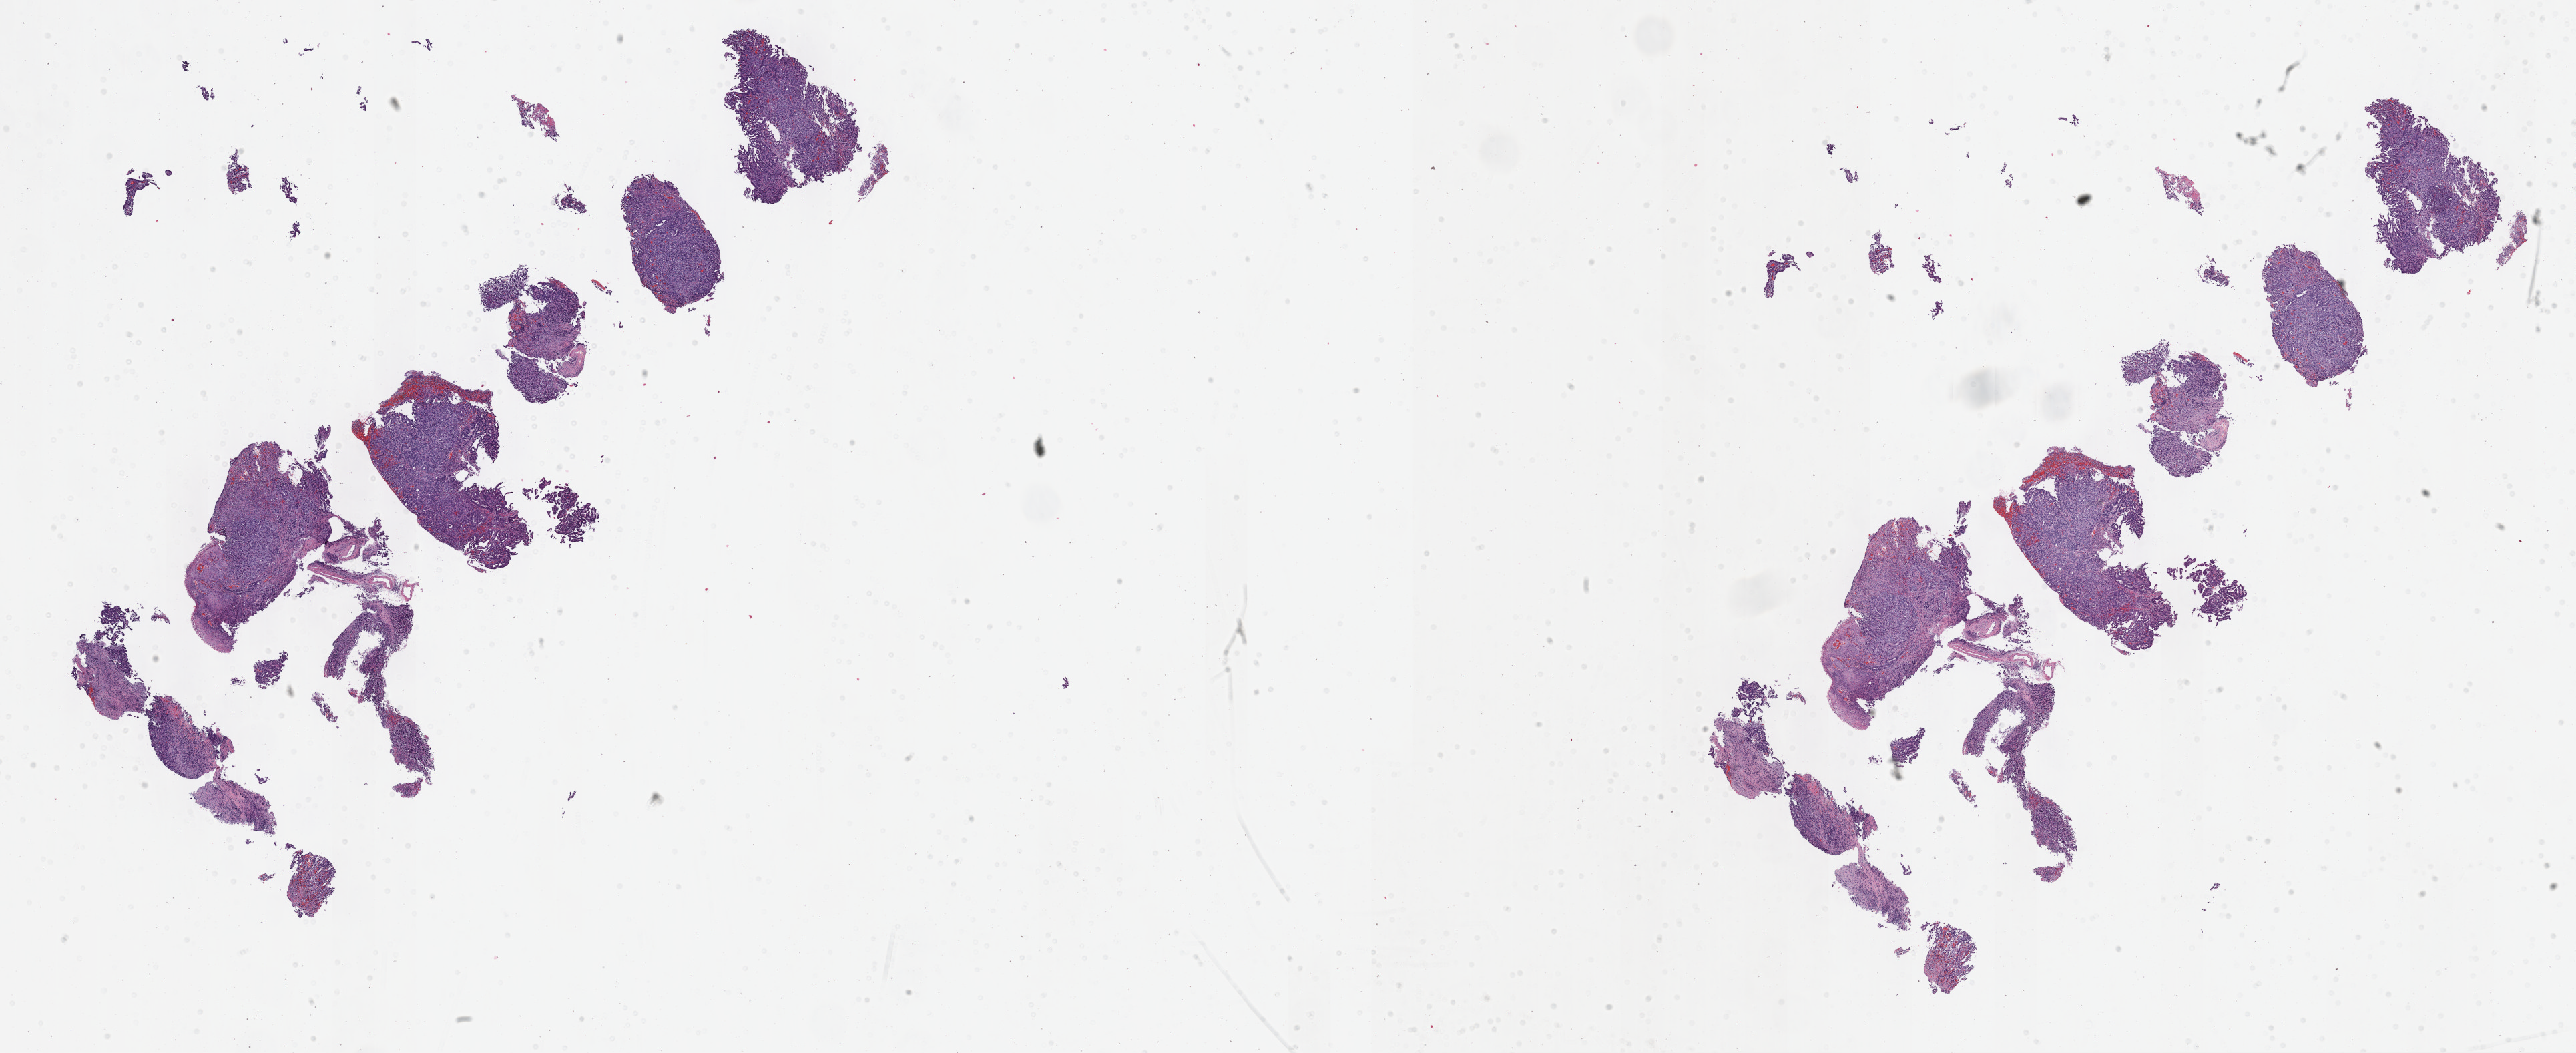
H&E whole-slide image, low-resolution overview of the scanned area, about 31.2 x 12.8 mm (acquisition: 40x scan). Formalin-fixed paraffin-embedded (FFPE) diagnostic section. Primary tumour sample from the esophagus. Male patient; age at initial diagnosis 60 years. Histologic grade: G3 (poorly differentiated). Composition of this section per pathologist review: tumour cells 80%, tumour nuclei 80%, normal cells 0%, stromal cells 20%, necrosis 0%. Infiltration values recorded for this section: lymphocyte infiltration 40%, monocyte infiltration 20%, neutrophil infiltration 20%.
* diagnosis: Adenocarcinoma, NOS (lower third of esophagus)